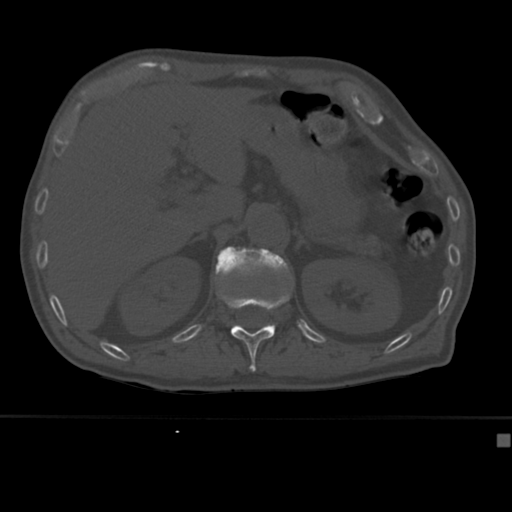
CT including the spine, one axial slice. Slice 185 of 430 in the series (ordered by position). Reconstruction kernel Br40s. 120 kVp. Bone window (W 1800 / L 400 HU). 1.5 mm slice thickness. 512 × 512 image matrix. Male patient, age 64 years. From the clinical record (not read from this slice): primary cancer: uterus; vertebrae with lytic lesions (as recorded): T1, T4, T5, T7, L5.
Annotated regions visible in this slice (semi-automatic segmentation, software-assisted and operator-edited):
- L1 vertebra: bounding box <215,246,292,280> (left, top, right, bottom; pixels)
- T12 vertebra: <217,289,291,372>